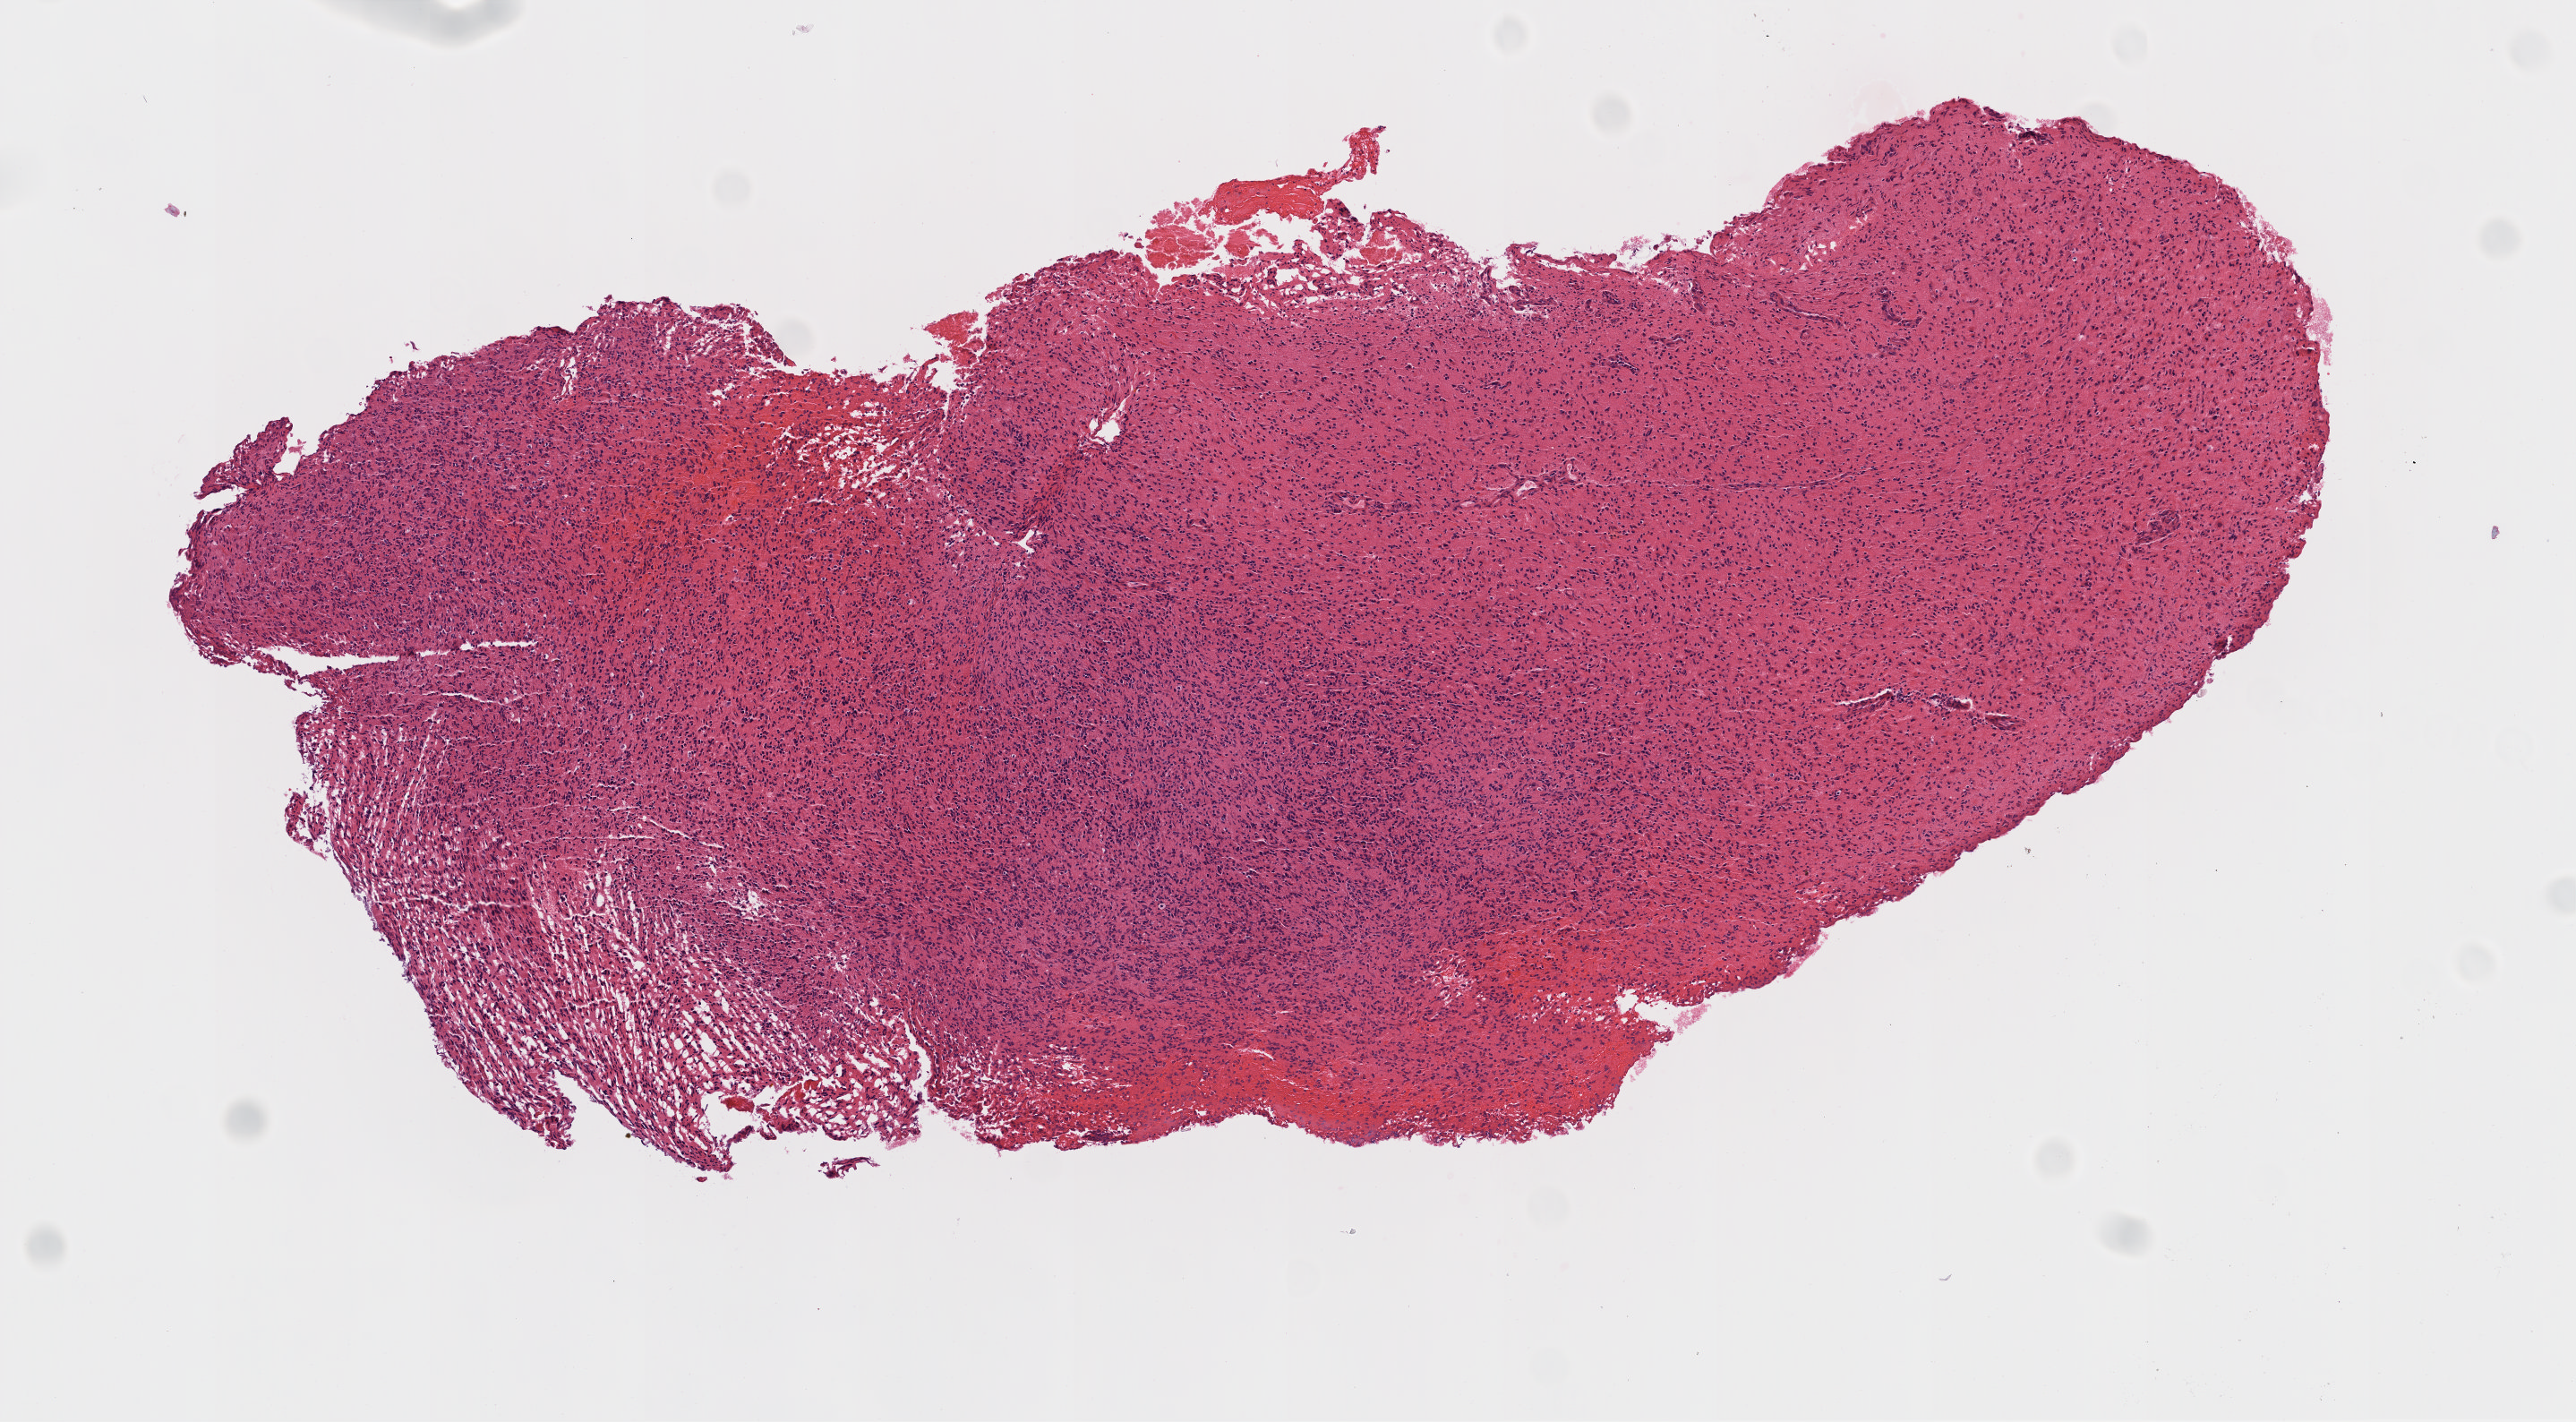
Digitized Hematoxylin and eosin (H&E) stained tissue section (whole slide) — shown as a low-resolution overview of the whole scanned area (about 5.8 x 3.2 mm); FFPE section; brain, primary tumour sample. Female, age 63 years at initial diagnosis.
Pathologic diagnosis: Glioblastoma.